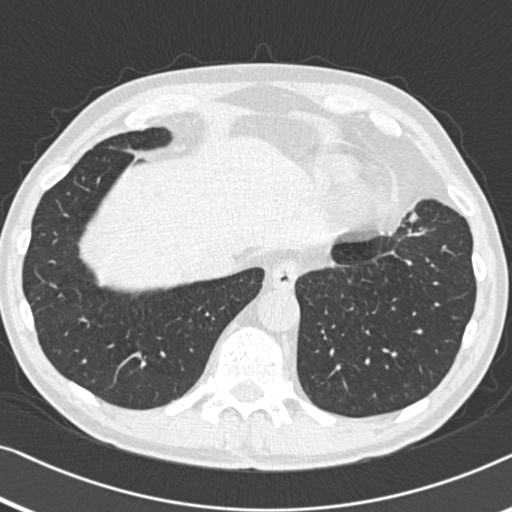
Low-dose screening chest CT, one axial slice; position 117 of 383 along the scan axis; reconstruction kernel B30f; lung window (W 1500 / L -600 HU); 1 mm slice thickness; 512 × 512 image matrix, field of view 332 × 332 mm.
Outlined on this slice (manually delineated by an expert):
- lesion 1 (tumor, upper lobe of left lung): bounding box <410,214,417,222> (left, top, right, bottom; pixels)